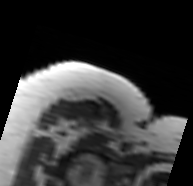
MRI of an extremity soft-tissue mass, one axial slice; position 67 of 91 along the scan axis; MR volume resampled by the dataset authors to the PET/CT grid (not the native acquisition matrix); 3.27 mm slice thickness; 193 × 186 image matrix. Female patient. From the clinical record (not read from this slice): histological type: malignant solitary fibrous tumor; grade: intermediate; site of the primary tumour: right thigh.
Annotated regions visible in this slice (expert contour drawn on MRI and transferred to this co-registered scan by the dataset authors):
- gross tumour volume including surrounding oedema: bounding box (x1, y1, x2, y2) in pixels: (53, 117, 112, 150)